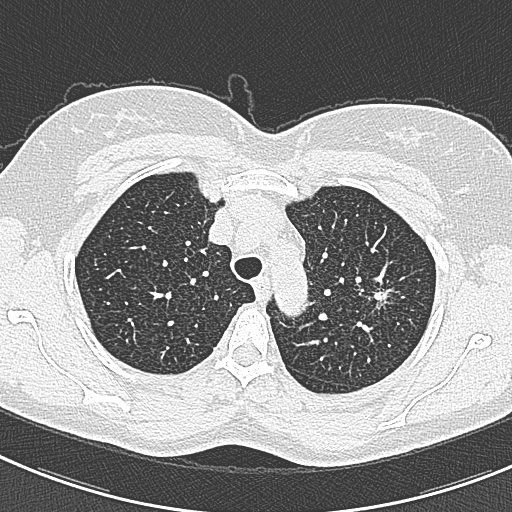
Low-dose screening chest CT, axial slice; baseline screening round; lung window (W 1500 / L -600 HU); lung (sharp) reconstruction kernel (B80f); 120 kVp. Female, age 57 years at enrolment. Current smoker at enrolment.
Expert reader's lesion annotation, bounding box <362,273,412,321> (left, top, right, bottom; pixels). The screening reader recorded 2 non-calcified nodules or masses ≥4 mm on this exam; which of them this box marks is not recorded. Later outcome: lung cancer diagnosed 198 days after this screen — adenocarcinoma, NOS, left upper lobe, well differentiated (G1), stage IA (AJCC 6th edition), 10 mm at pathology.